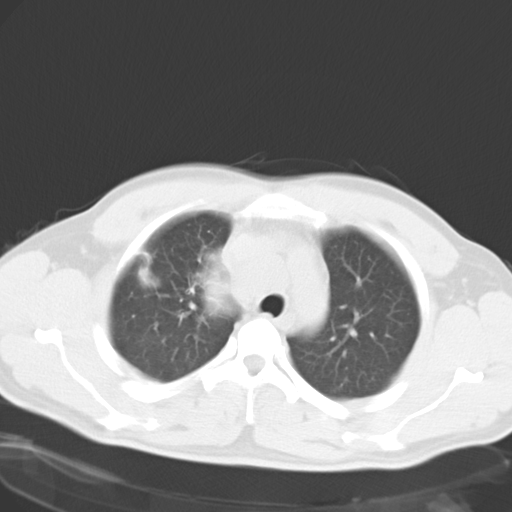
Chest CT, one axial slice. Position 21 of 27 along the scan axis. 120 kVp. Lung window (W 1500 / L -600 HU). 512 × 512 image matrix, field of view 346 × 346 mm. Male patient, age 32 years. From the clinical record (not read from this slice): clinical TNM (as recorded): T4 N3 M0; histopathological grade: G3.
Structures marked on this image (rectangle marked by the reading radiologist):
- lung tumour (recorded histology: small cell carcinoma): bounding box <194,242,242,320> (left, top, right, bottom; pixels)